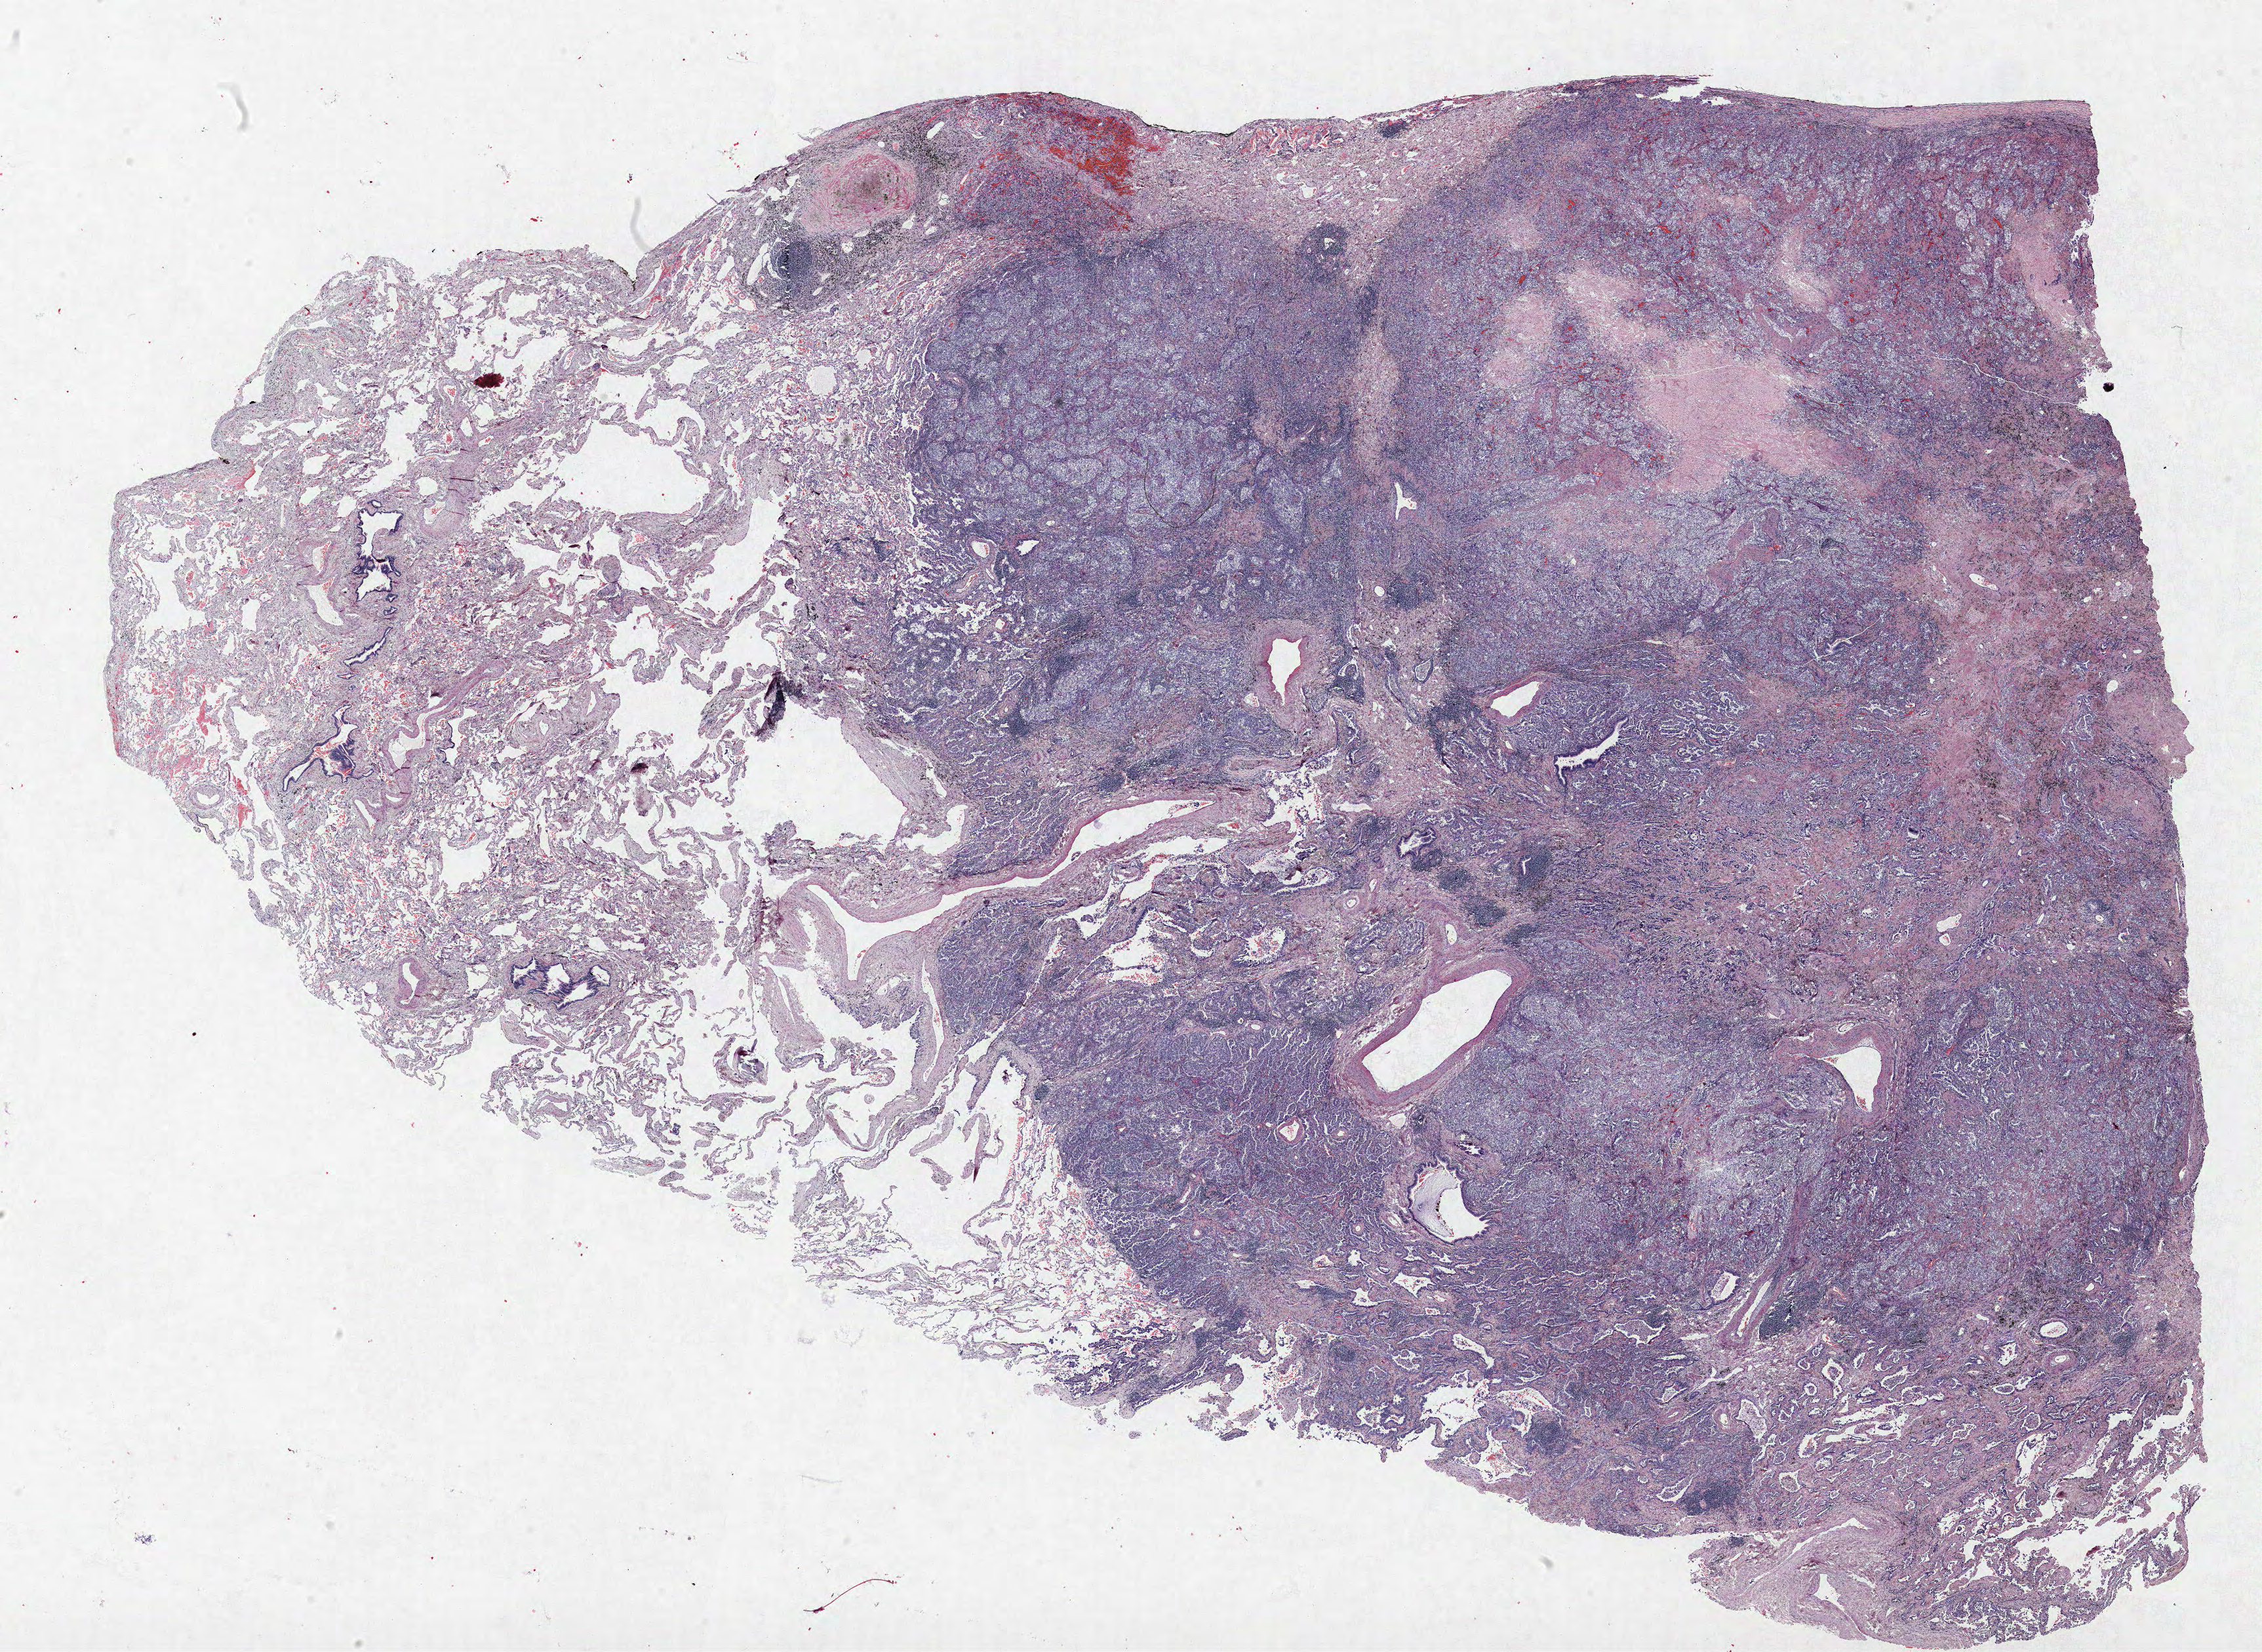
Whole-slide histology image, H&E-stained — a low-resolution overview of the entire scanned area, about 27.6 x 20.2 mm; formalin-fixed paraffin-embedded (FFPE) section; lung. Female, age 70 at enrolment. Grade: moderately differentiated (G2).
Primary tumour location (clinical record): left upper lobe. Participant's lung-cancer diagnosis: Clear cell adenocarcinoma, NOS (ICD-O-3 8310/3). Tumour size (pathology): 41 mm. Stage (AJCC 6th edition): IB.